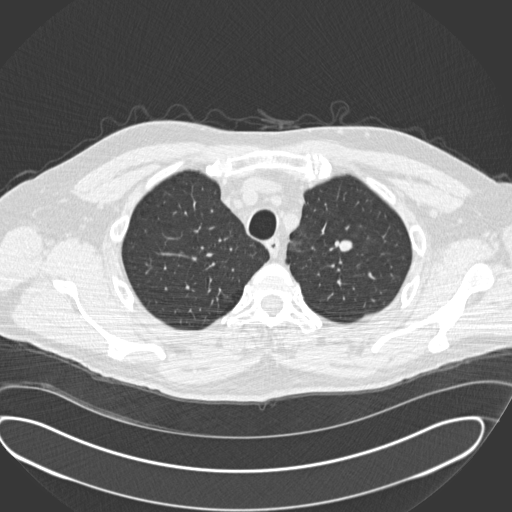
Chest CT (low-dose screening protocol), one axial image; second annual screen; lung window (W 1500 / L -600 HU); standard (soft-tissue) reconstruction kernel (B30f); 120 kVp; 512 × 512 image matrix. Male participant, aged 56 years at enrolment. Current smoker at enrolment.
Expert-annotated lung lesion, bounding box [x1, y1, x2, y2] px = [313, 227, 370, 270]. Screening reader's record for this exam: no non-calcified nodule ≥4 mm recorded. Later outcome: lung cancer diagnosed 520 days after this screen (after the third annual screen) — neuroendocrine carcinoma, NOS, left upper lobe, well differentiated (G1), stage IA (AJCC 6th edition), 20 mm at pathology.